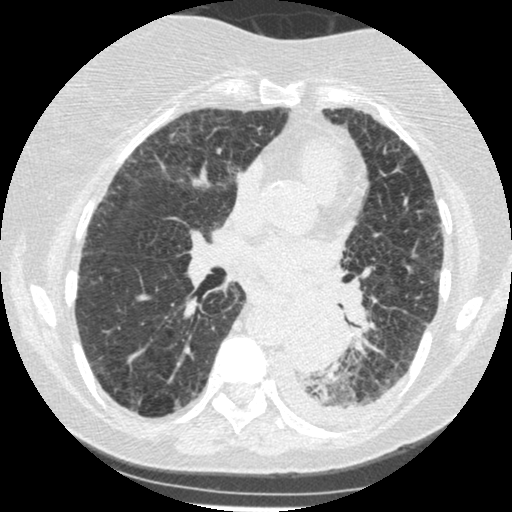
Chest CT (low-dose screening protocol), one axial image. Third screening round (two years after baseline). Lung window (W 1500 / L -600 HU). 1.25 mm slice thickness. Slice 217 of 341 in the series. 512 × 512 image matrix. Female participant, aged 60 years at enrolment. Former smoker at enrolment.
Expert reader's lesion annotation, bounding box <273,305,342,374> (left, top, right, bottom; pixels). The exam's reader record, not a measurement of the box and not confirmed to be the same lesion: non-calcified nodule or mass ≥4 mm, left lower lobe, 54 × 38 mm, smooth margins, soft tissue attenuation, pre-existing on the prior screen: yes; interval growth: yes. Participant outcome: lung cancer diagnosed 15 days after this screen — small cell carcinoma, NOS, left lower lobe, undifferentiated (G4), stage IV (AJCC 6th edition), 69 mm at pathology.